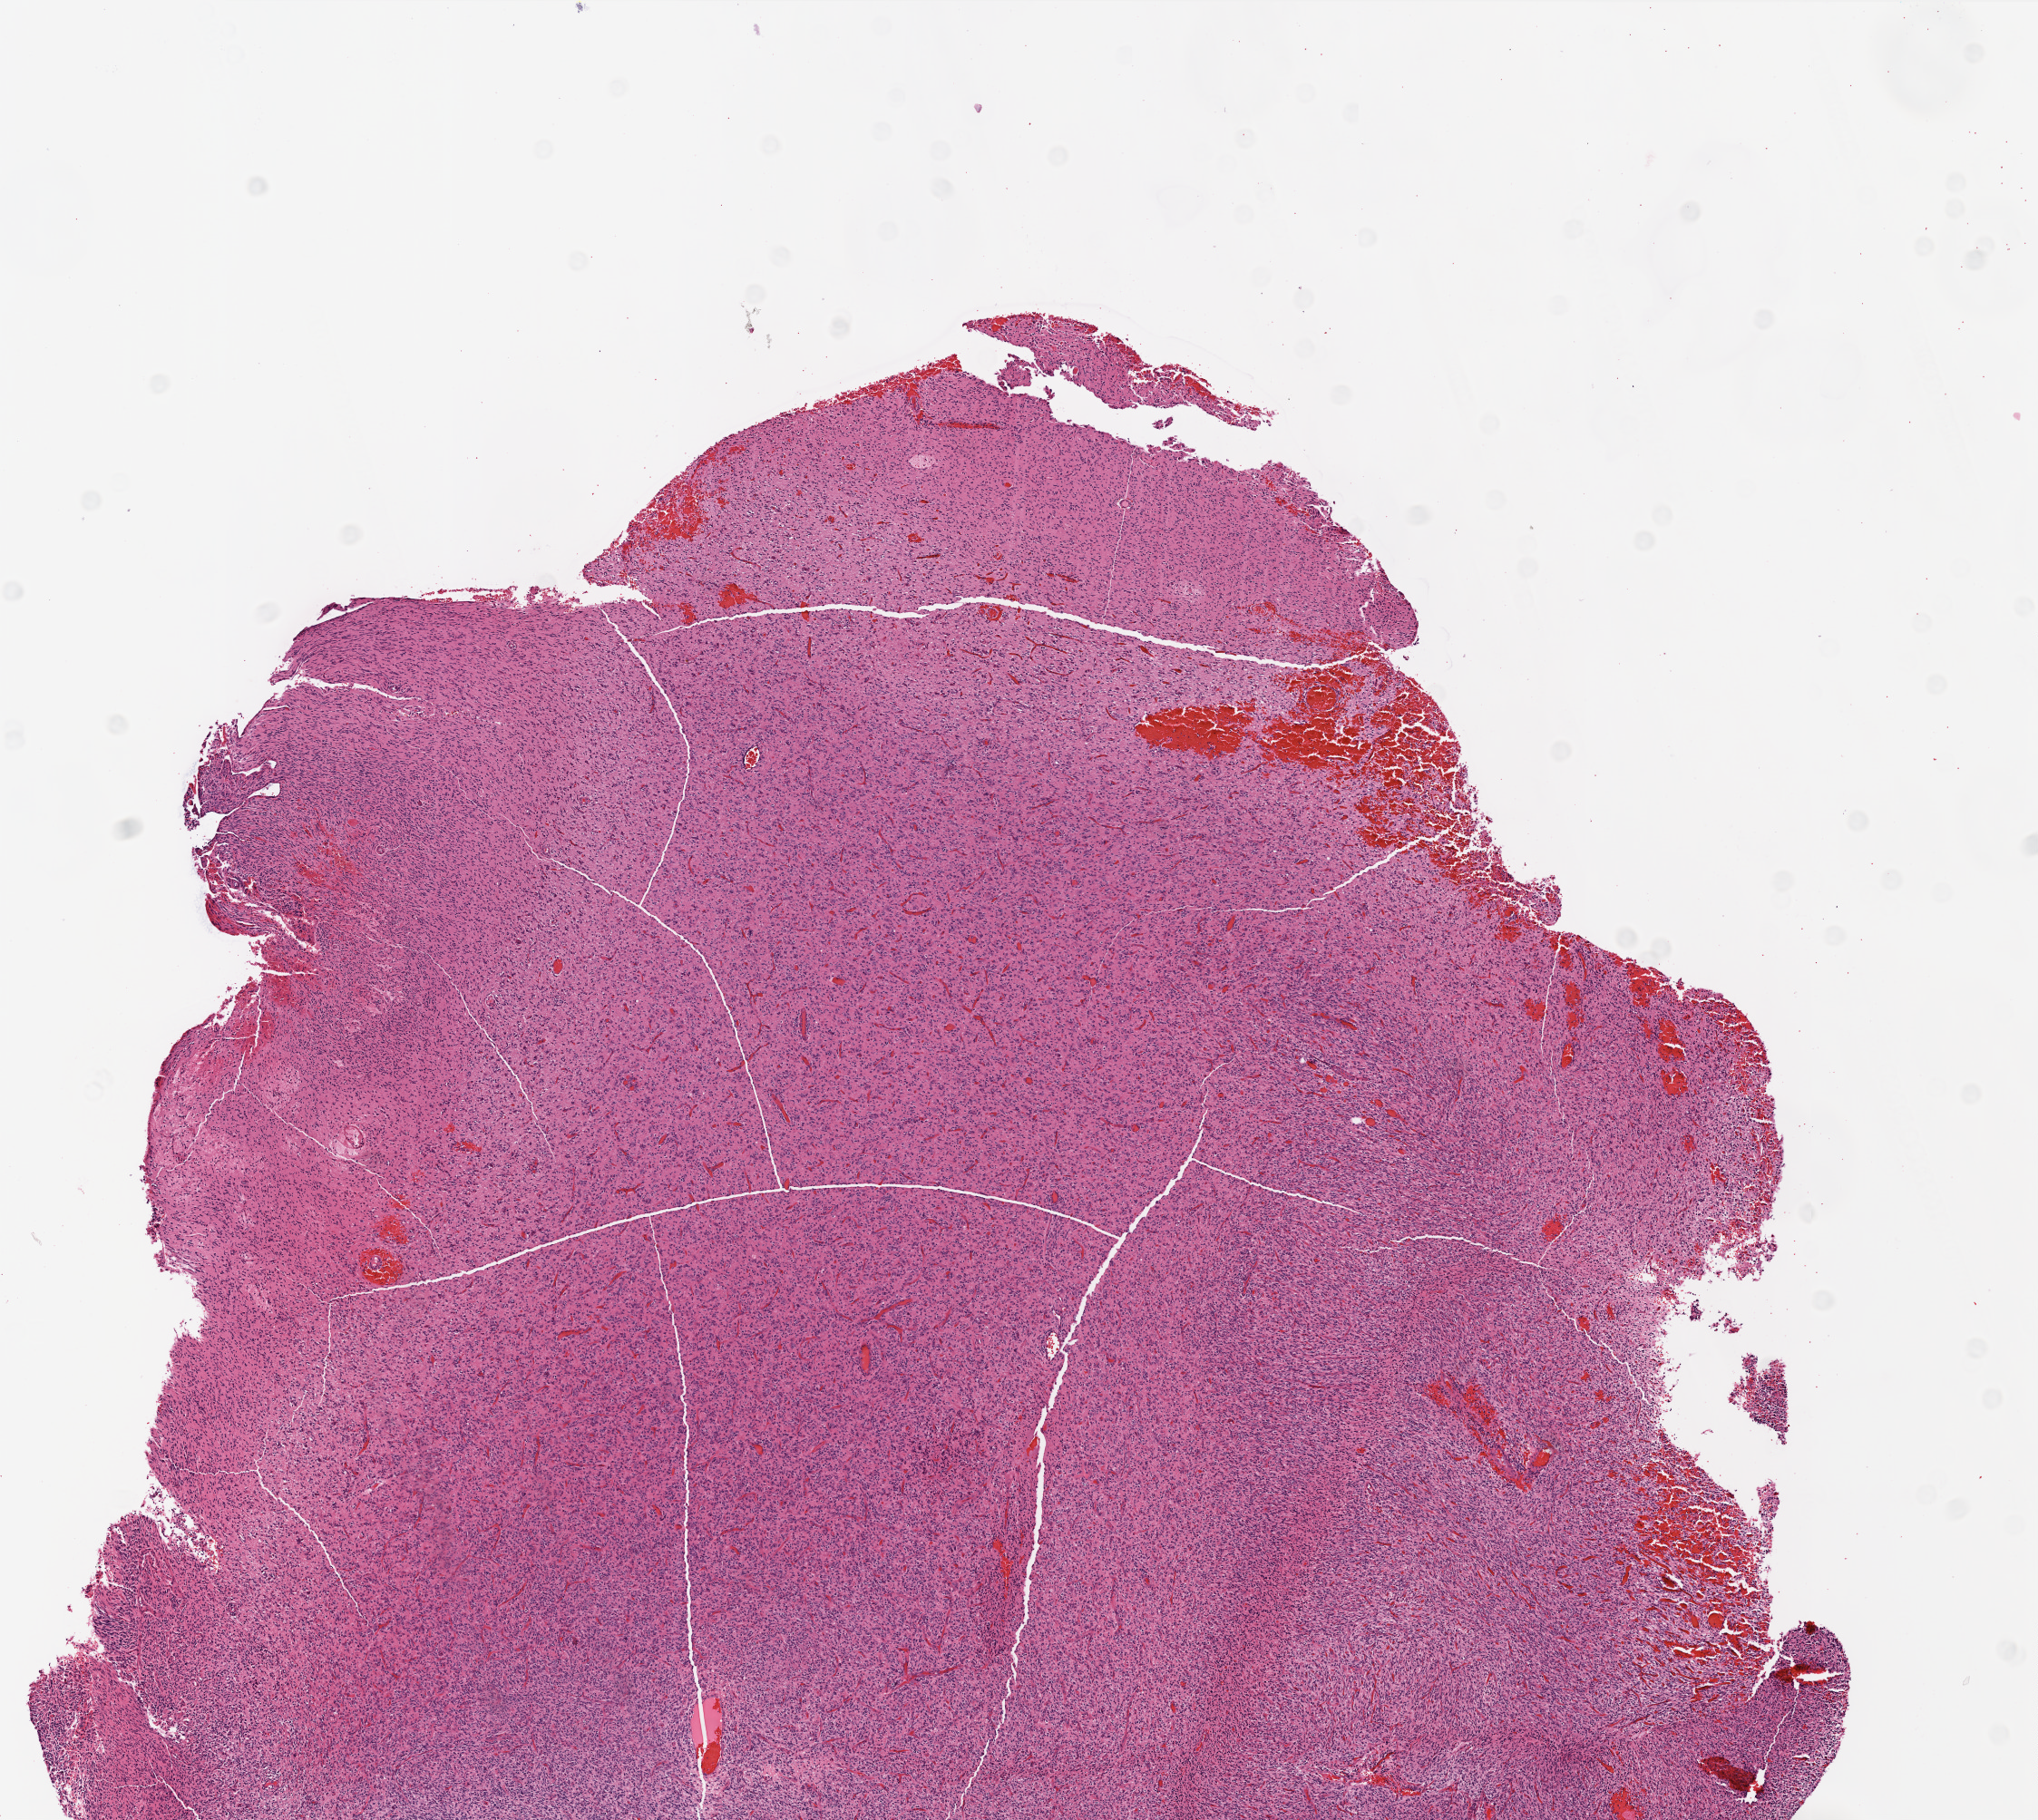
Digitized H&E tissue section (whole slide), low-resolution overview of the scanned area, about 9.0 x 8.0 mm (acquisition: 20x scan); FFPE section; sample: primary tumour, brain. Patient: male, age at initial diagnosis 47 years.
Diagnosis: Glioblastoma.